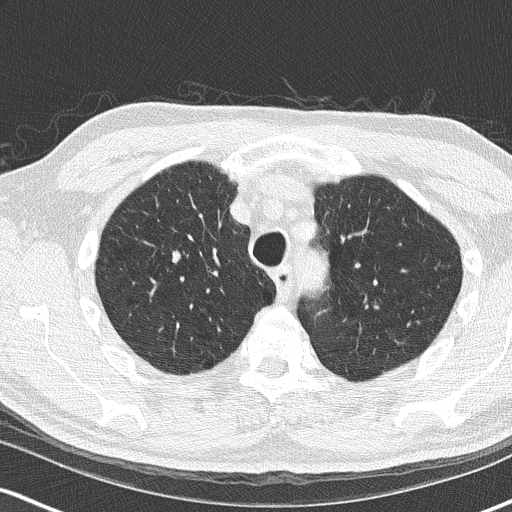
Chest CT (low-dose screening protocol), one axial image; second screening round (one year after baseline); lung window (W 1500 / L -600 HU); 2 mm slice thickness; lung (sharp) reconstruction kernel (B50f); 120 kVp. Male, age 68 years at enrolment. Current smoker at enrolment.
Expert-annotated lung lesion, box from (x=151, y=233) to (x=215, y=294) px. Screening reader's record for this exam (one nodule recorded; not confirmed to be the boxed lesion): non-calcified nodule or mass ≥4 mm, right upper lobe, 18 × 15 mm, smooth margins, soft tissue attenuation, pre-existing on the prior screen: no. Lung cancer was diagnosed 136 days after this screen: small cell carcinoma, NOS, right upper lobe, stage IIIB (AJCC 6th edition), 20 mm at pathology.